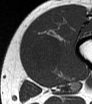
MRI of an extremity soft-tissue mass, one axial slice. Position 14 of 62 along the scan axis. MR volume resampled by the dataset authors to the PET/CT grid (not the native acquisition matrix). 3.27 mm slice thickness. 92 × 104 image matrix, field of view 90 × 102 mm. Male patient. Case-level facts recorded for this patient, not image findings: histological type: mixoid liposarcoma; grade: low; site of the primary tumour: left thigh.
Outlined on this slice (expert contour drawn on MRI and transferred to this co-registered scan by the dataset authors):
- gross tumour volume (mass): bounding box [x1, y1, x2, y2] px = [28, 35, 63, 73]